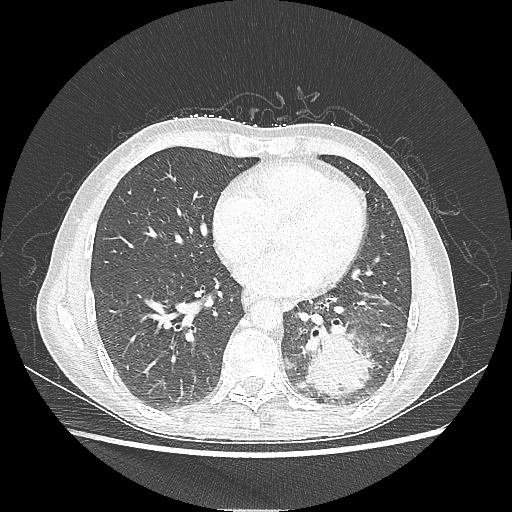
Chest CT, one axial slice. Position 89 of 220 along the scan axis. Reconstruction kernel LUNG. 80 kVp. Lung window (W 1500 / L -600 HU). 1.25 mm slice thickness. 512 × 512 image matrix, field of view 360 × 360 mm. Female patient, age 53 years. From the clinical record (not read from this slice): clinical TNM (as recorded): T3 N0 M0.
Annotated regions visible in this slice (bounding box drawn by a radiologist):
- lung tumour (recorded histology: adenocarcinoma): bounding box (x1, y1, x2, y2) in pixels: (301, 325, 373, 400)